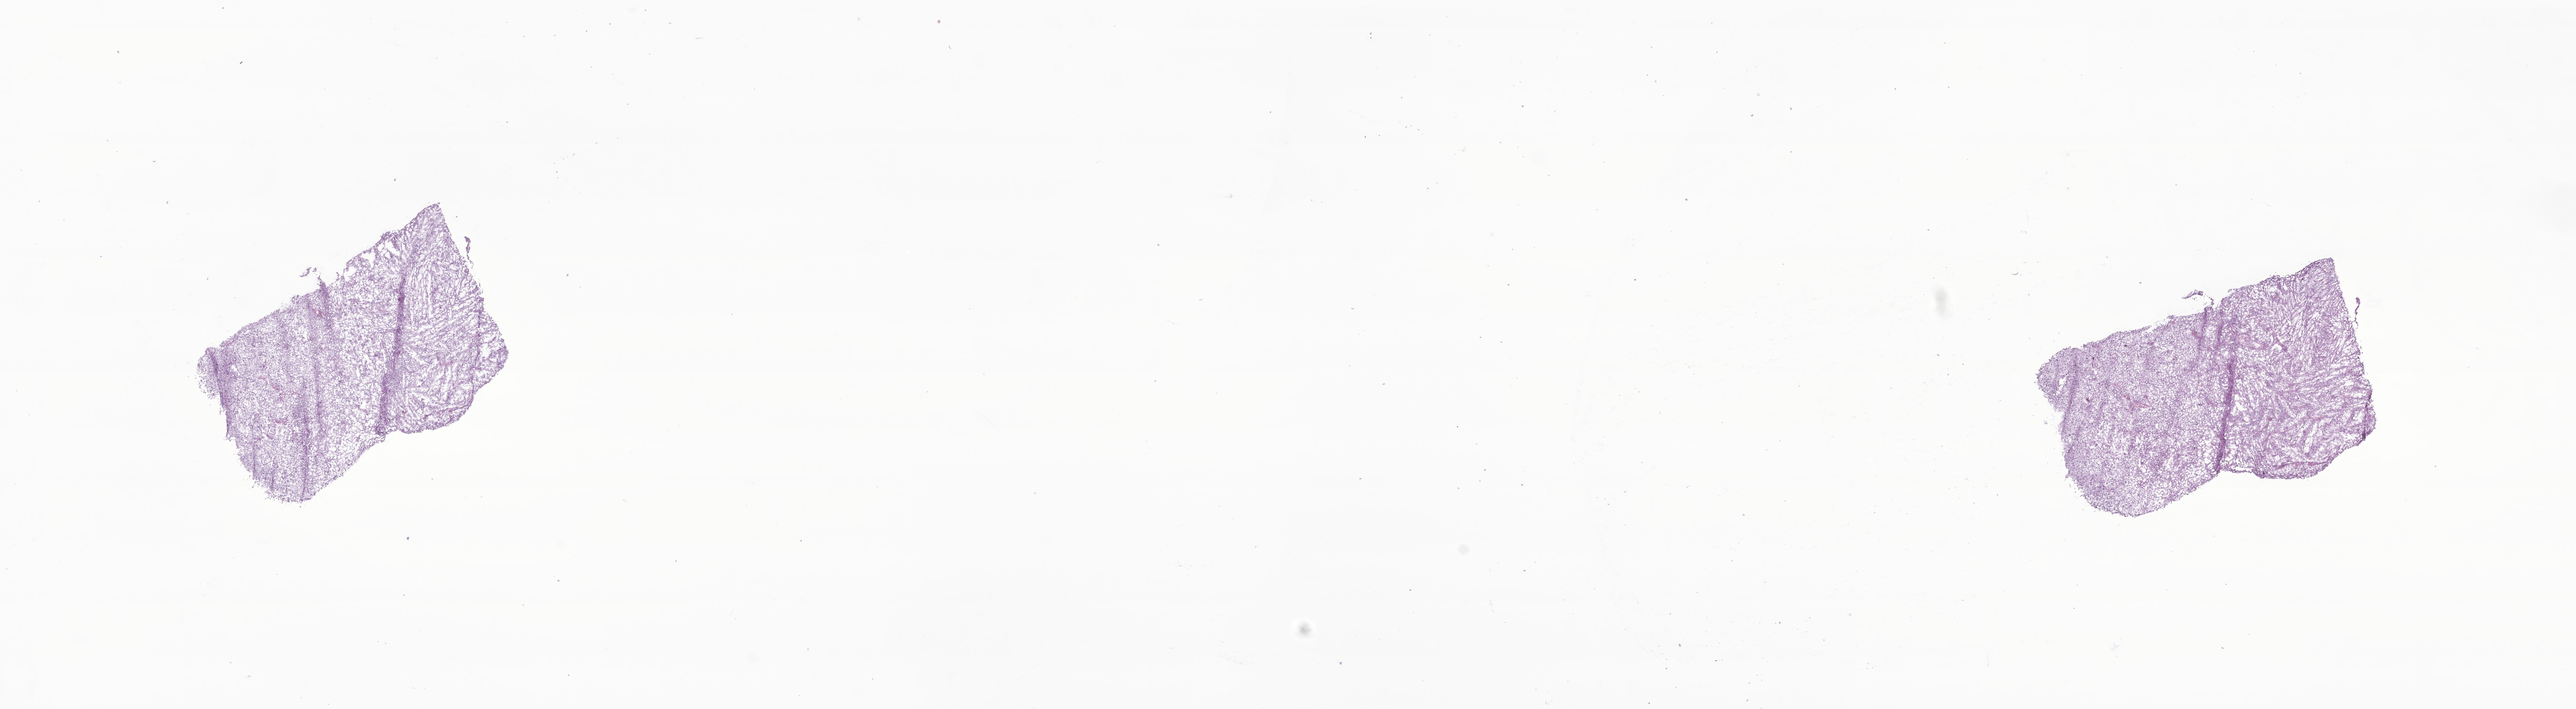
Haematoxylin and eosin whole-slide image of tumor tissue from the brain — a low-resolution overview of the entire scanned area, about 24.0 x 6.6 mm; frozen section (OCT-embedded). Female patient, age 149 months (12 years 5 months).
• diagnosis (ICD-O-3 morphology term): Glioma, malignant